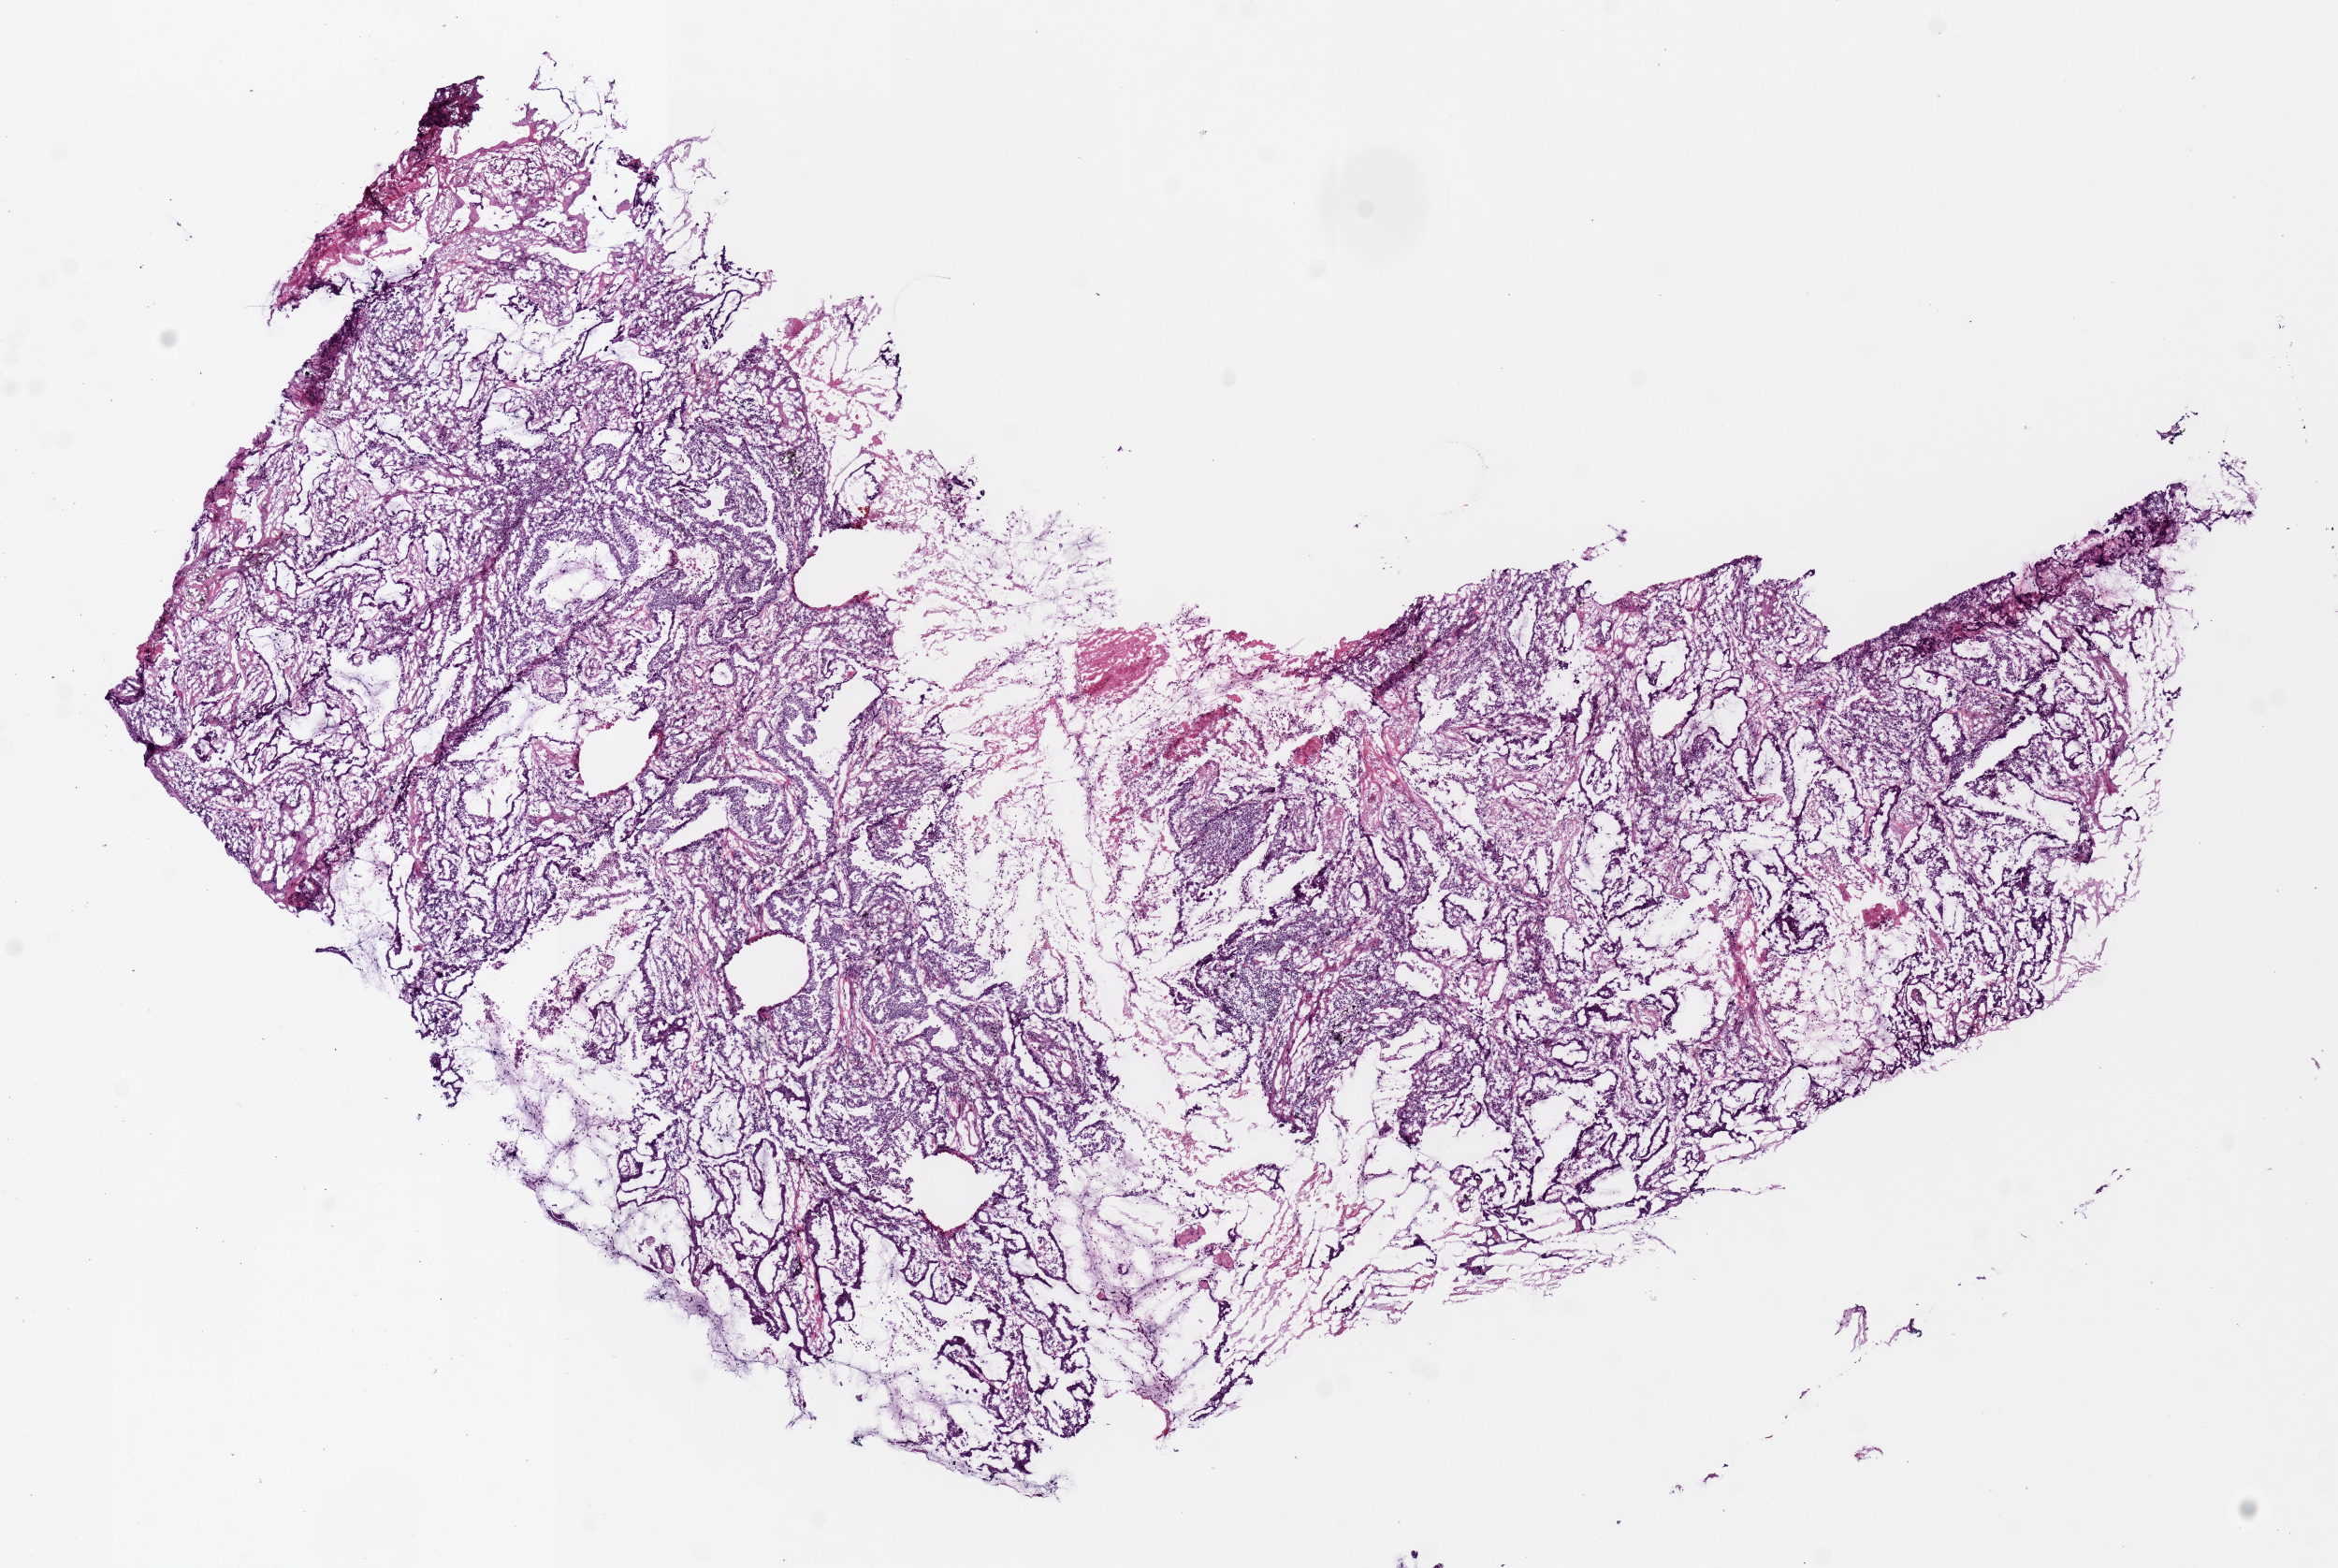
Digitized H&E-stained tissue section (whole slide) — low-resolution overview of the scanned area, about 9.9 x 6.7 mm; frozen section from the top of the tissue portion; lung, primary tumour sample. Female, age 60 years at initial diagnosis. Pathologist review of this section (percent, as recorded): tumour nuclei 65%, necrosis 0%.
• AJCC pathologic stage: IIA (7th edition)
• pathologic diagnosis: Mucinous adenocarcinoma (upper lobe, lung)